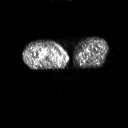
FDG PET of an extremity soft-tissue mass (from a PET/CT study), one axial slice; position 236 of 311 along the scan axis; 128 × 128 image matrix, field of view 700 × 700 mm. Patient: male, 50 years. Case-level facts recorded for this patient, not image findings: histological type: undifferentiated - pleiomorphic; grade: high; site of the primary tumour: right thigh.
Outlined on this slice (expert contour drawn on MRI and transferred to this co-registered scan by the dataset authors):
- gross tumour volume including surrounding oedema: bounding box [x1, y1, x2, y2] px = [42, 51, 55, 58]